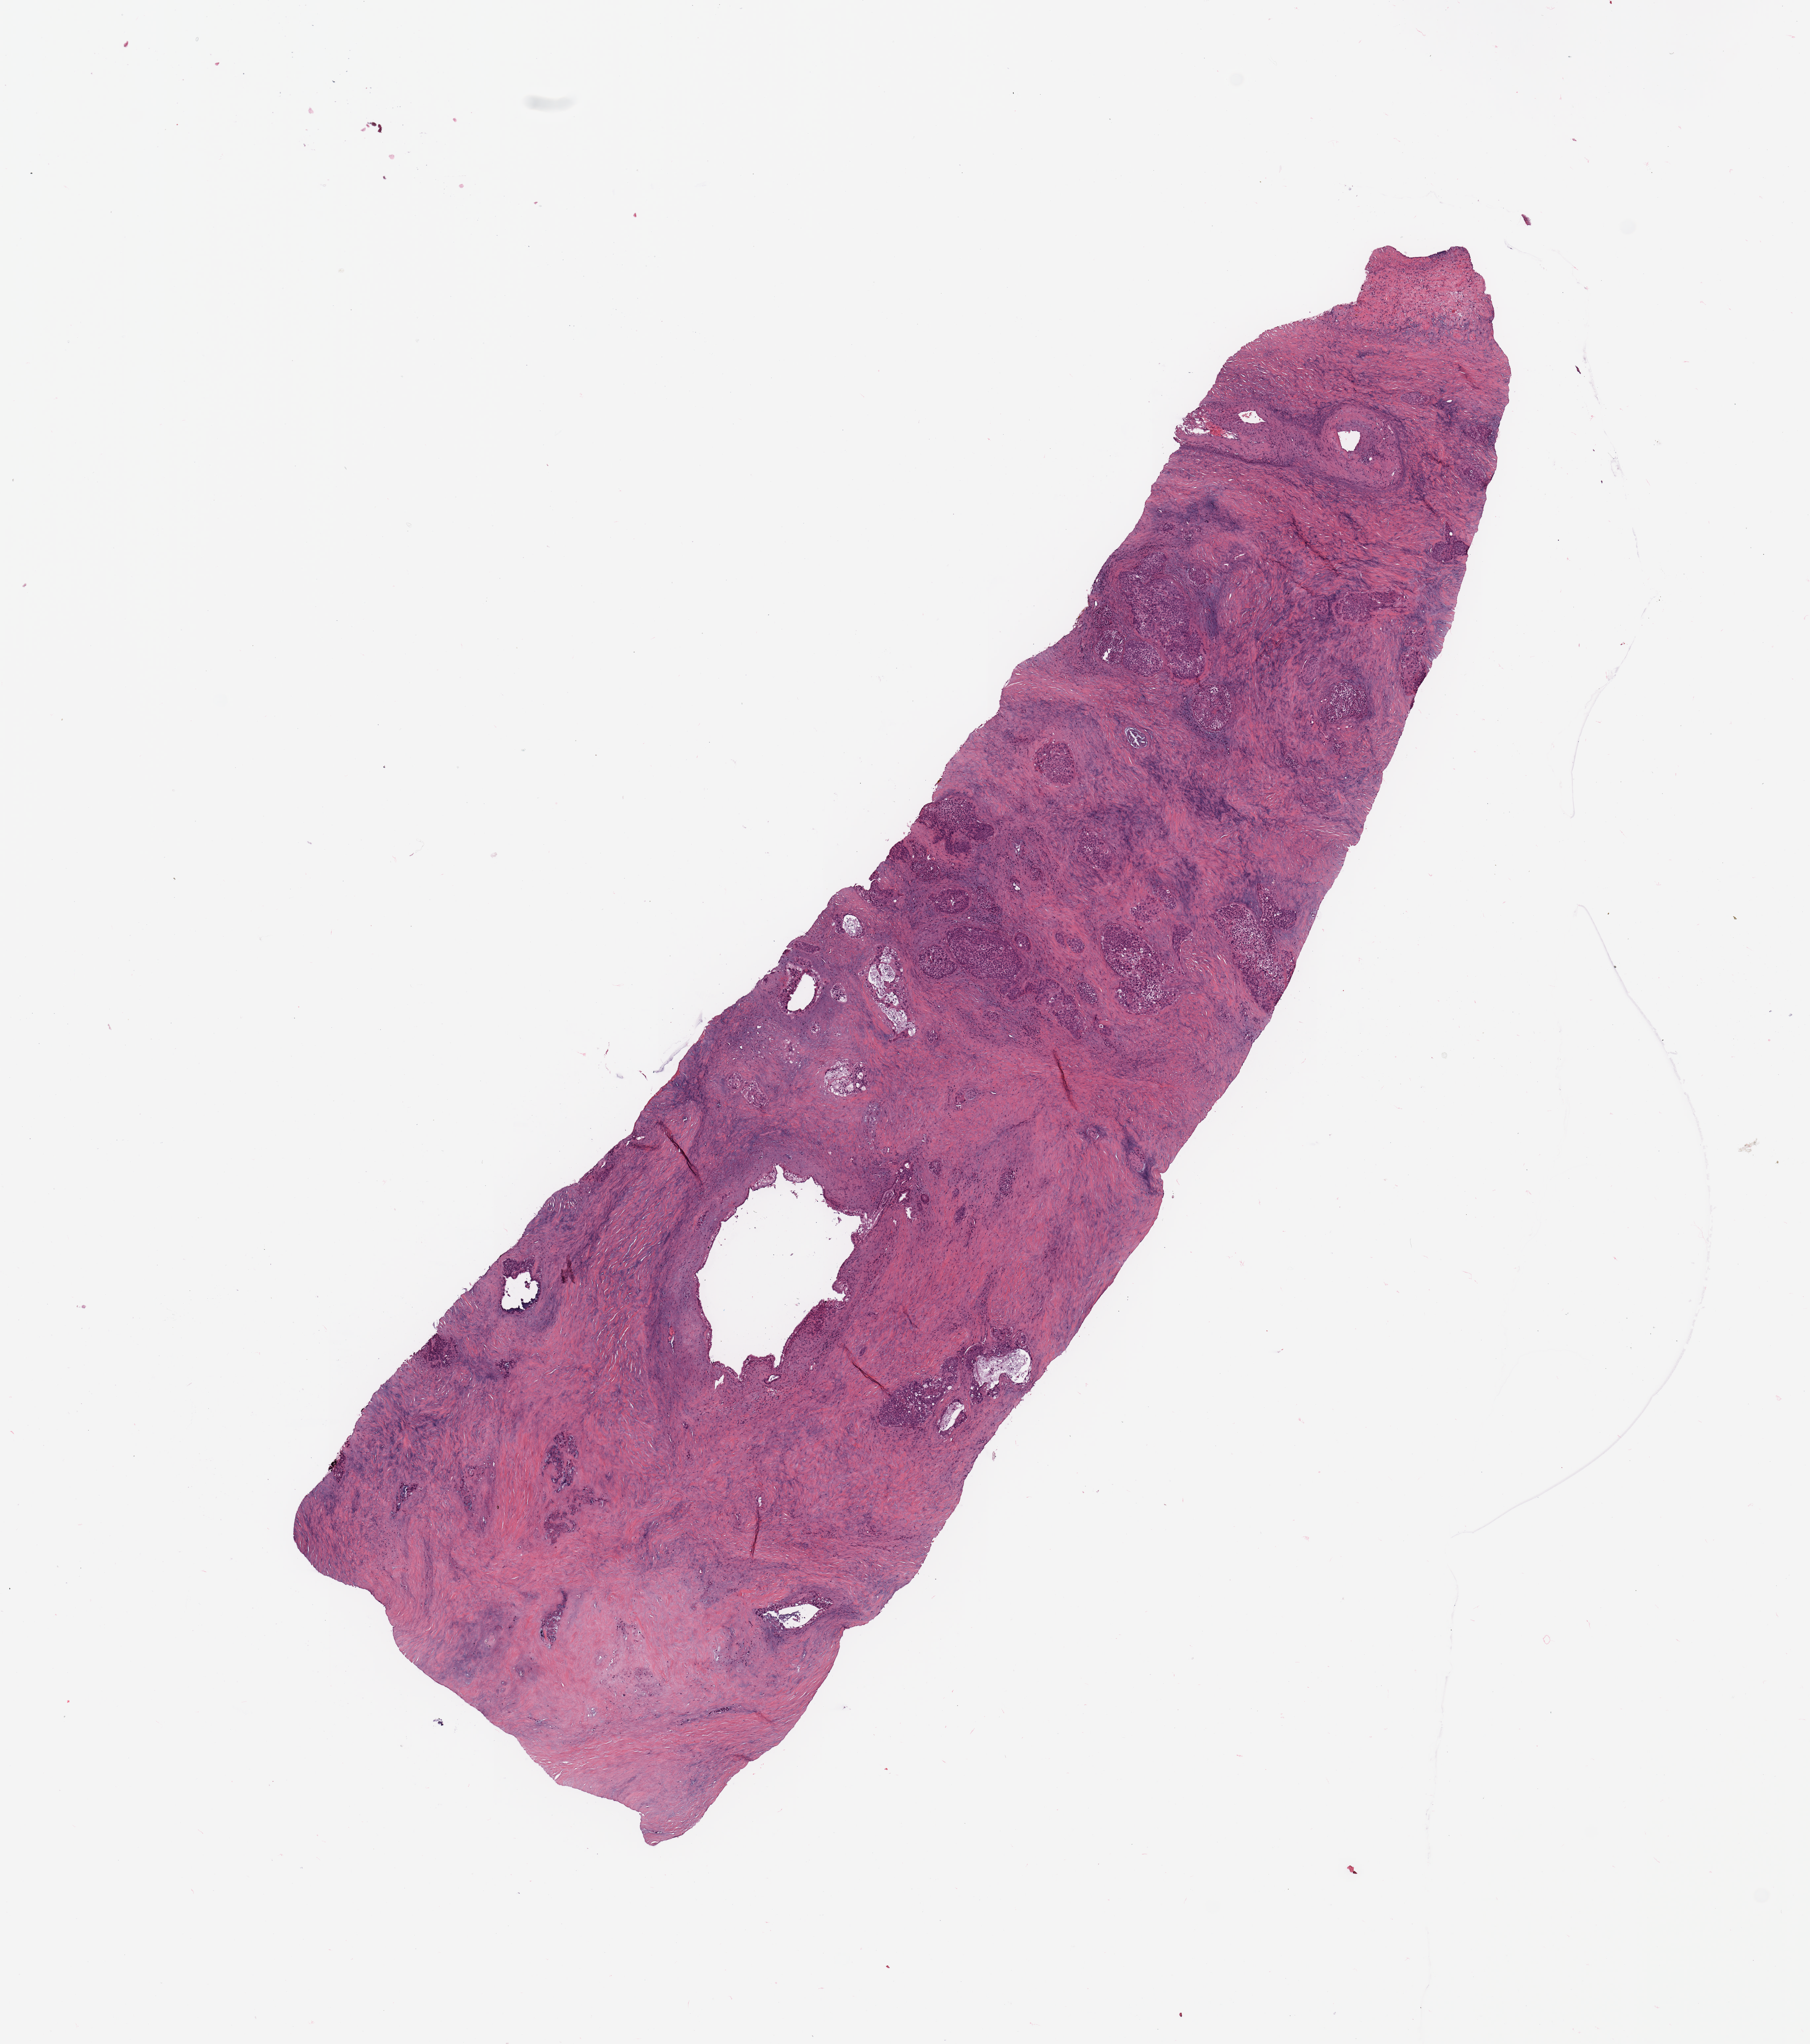
Digitized Hematoxylin and eosin (H&E) stained tissue section (whole slide), a low-resolution overview of the entire scanned area, about 10.8 x 12.2 mm (acquisition: 20x scan); tumour tissue sample, pancreas. Patient: male, age 69 years.
Diagnosis: Infiltrating duct carcinoma, NOS.